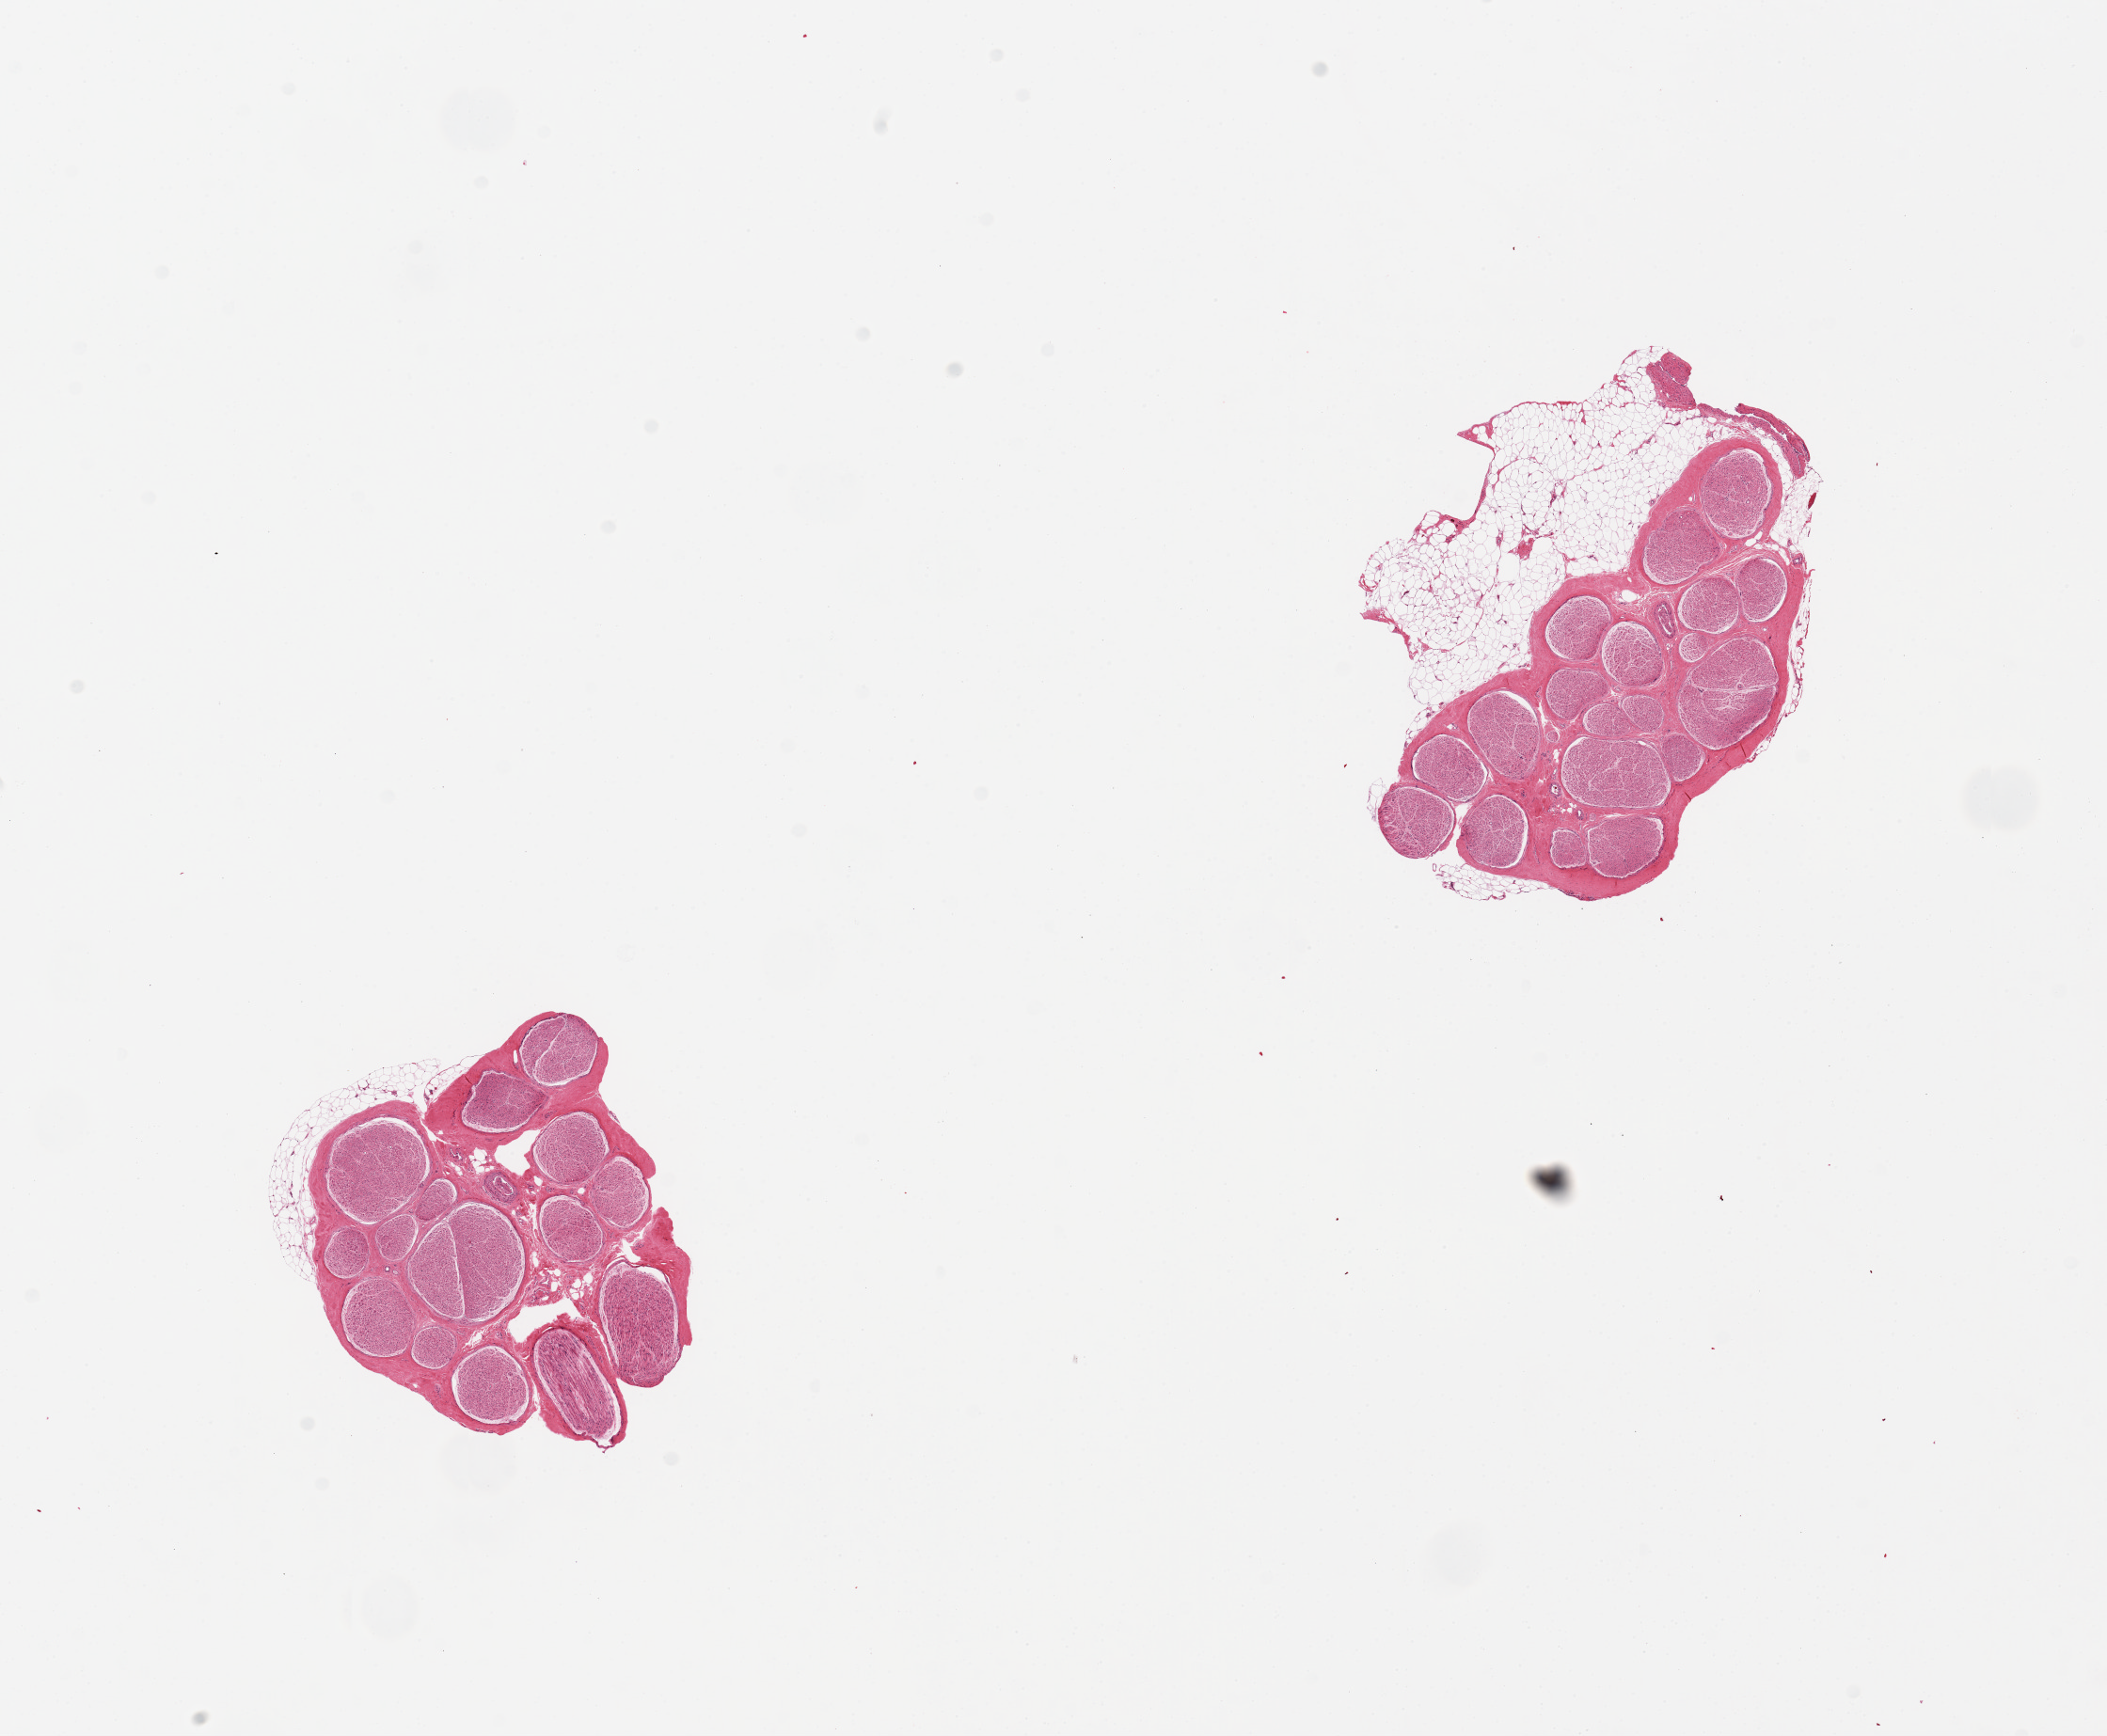
Digitized haematoxylin and eosin-stained section — a low-resolution overview of the entire scanned area, about 17.7 x 14.6 mm (acquisition: 20x scan). PAXgene-fixed, paraffin-embedded tissue. Target tissue: tibial nerve. Tissue donor sample.
Pathologist's review note for this sample: 2 pieces; nubbins of adherent fat up to ~1mm.